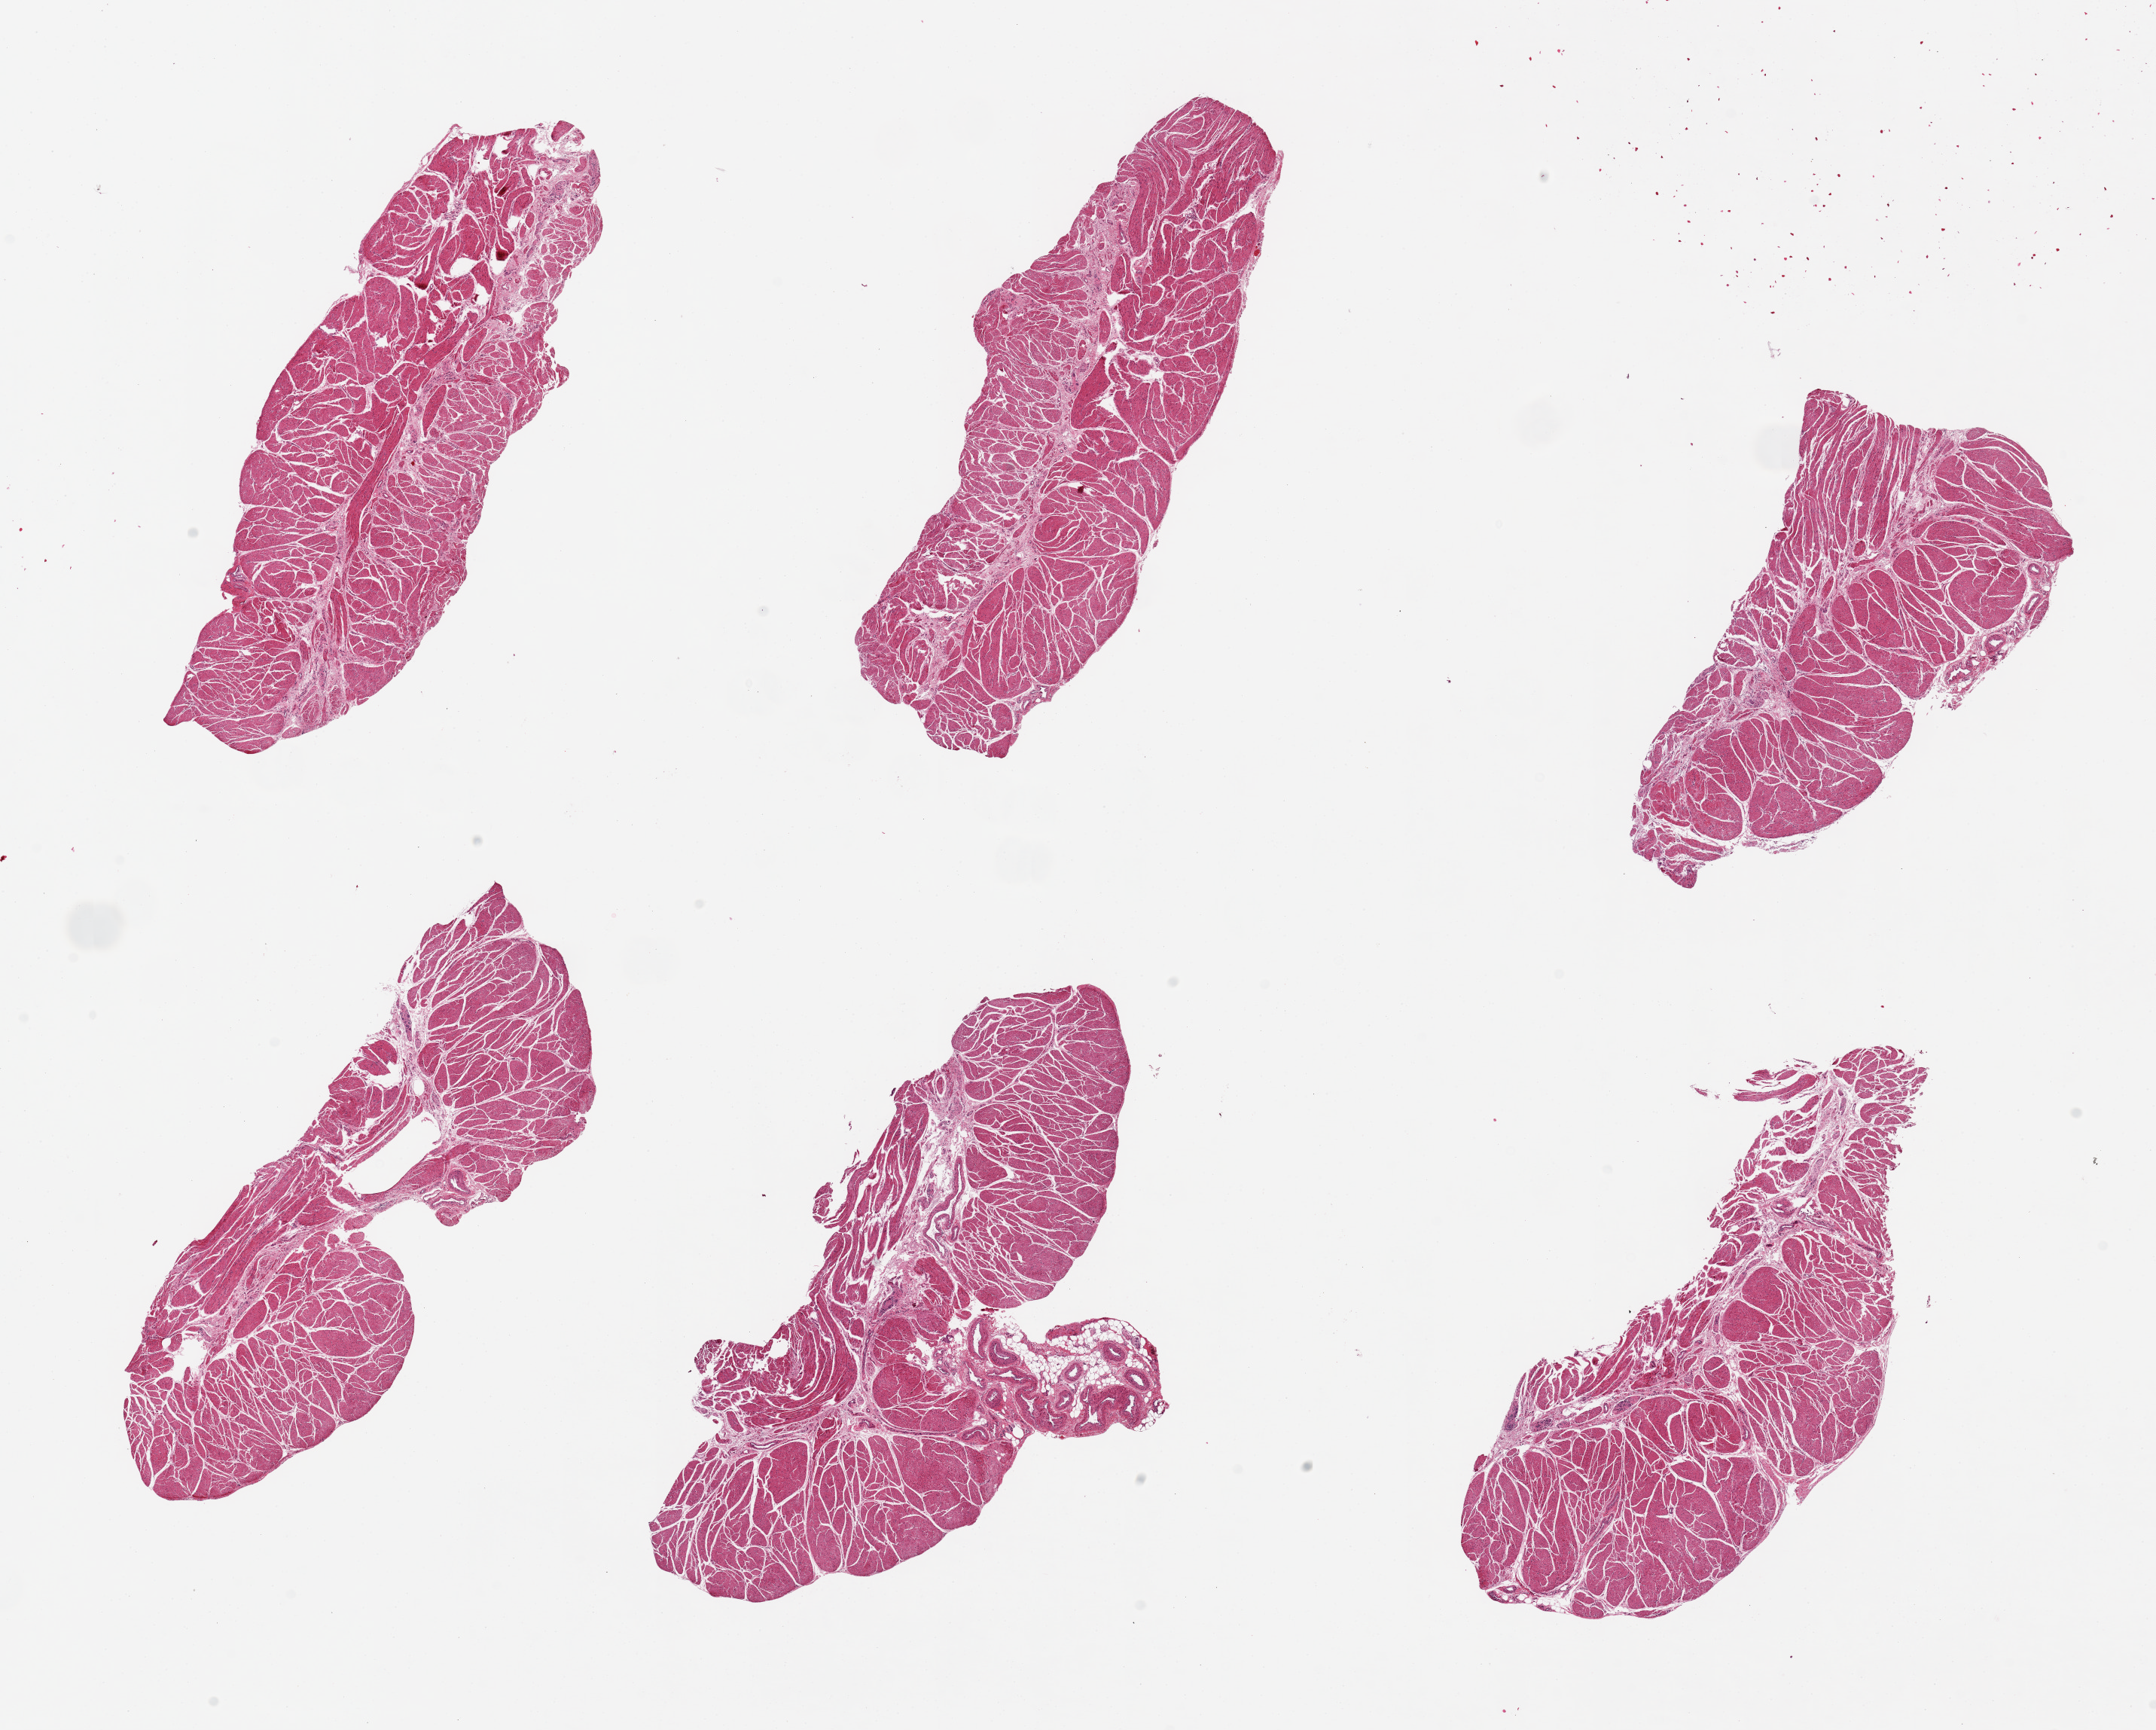
Digitized H&E-stained section, a low-resolution overview of the entire scanned area, about 22.6 x 18.2 mm (slide scanned at 20x); PAXgene-fixed, paraffin-embedded tissue; sampled site (target tissue): esophageal muscle; tissue donor sample. Male donor.
Pathologist's review note for this sample: 6 pieces, up to 7x5mm; well dissected; prominent focus of ganglion cell marked.